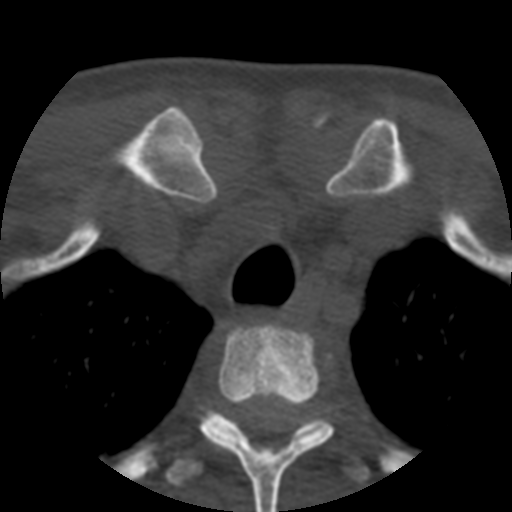
CT including the spine, one axial slice; slice 427 of 508 in the series (ordered by position); reconstruction kernel STANDARD; bone window (W 1800 / L 400 HU); 1.25 mm slice thickness; 512 × 512 image matrix, field of view 160 × 160 mm. Patient age 57 years. Case-level facts recorded for this patient, not image findings: primary cancer: prostate.
Outlined on this slice (semi-automatically segmented with operator editing):
- T2 vertebra: bounding box [x1, y1, x2, y2] px = [199, 325, 333, 512]
- T3 vertebra: [166, 411, 369, 486]